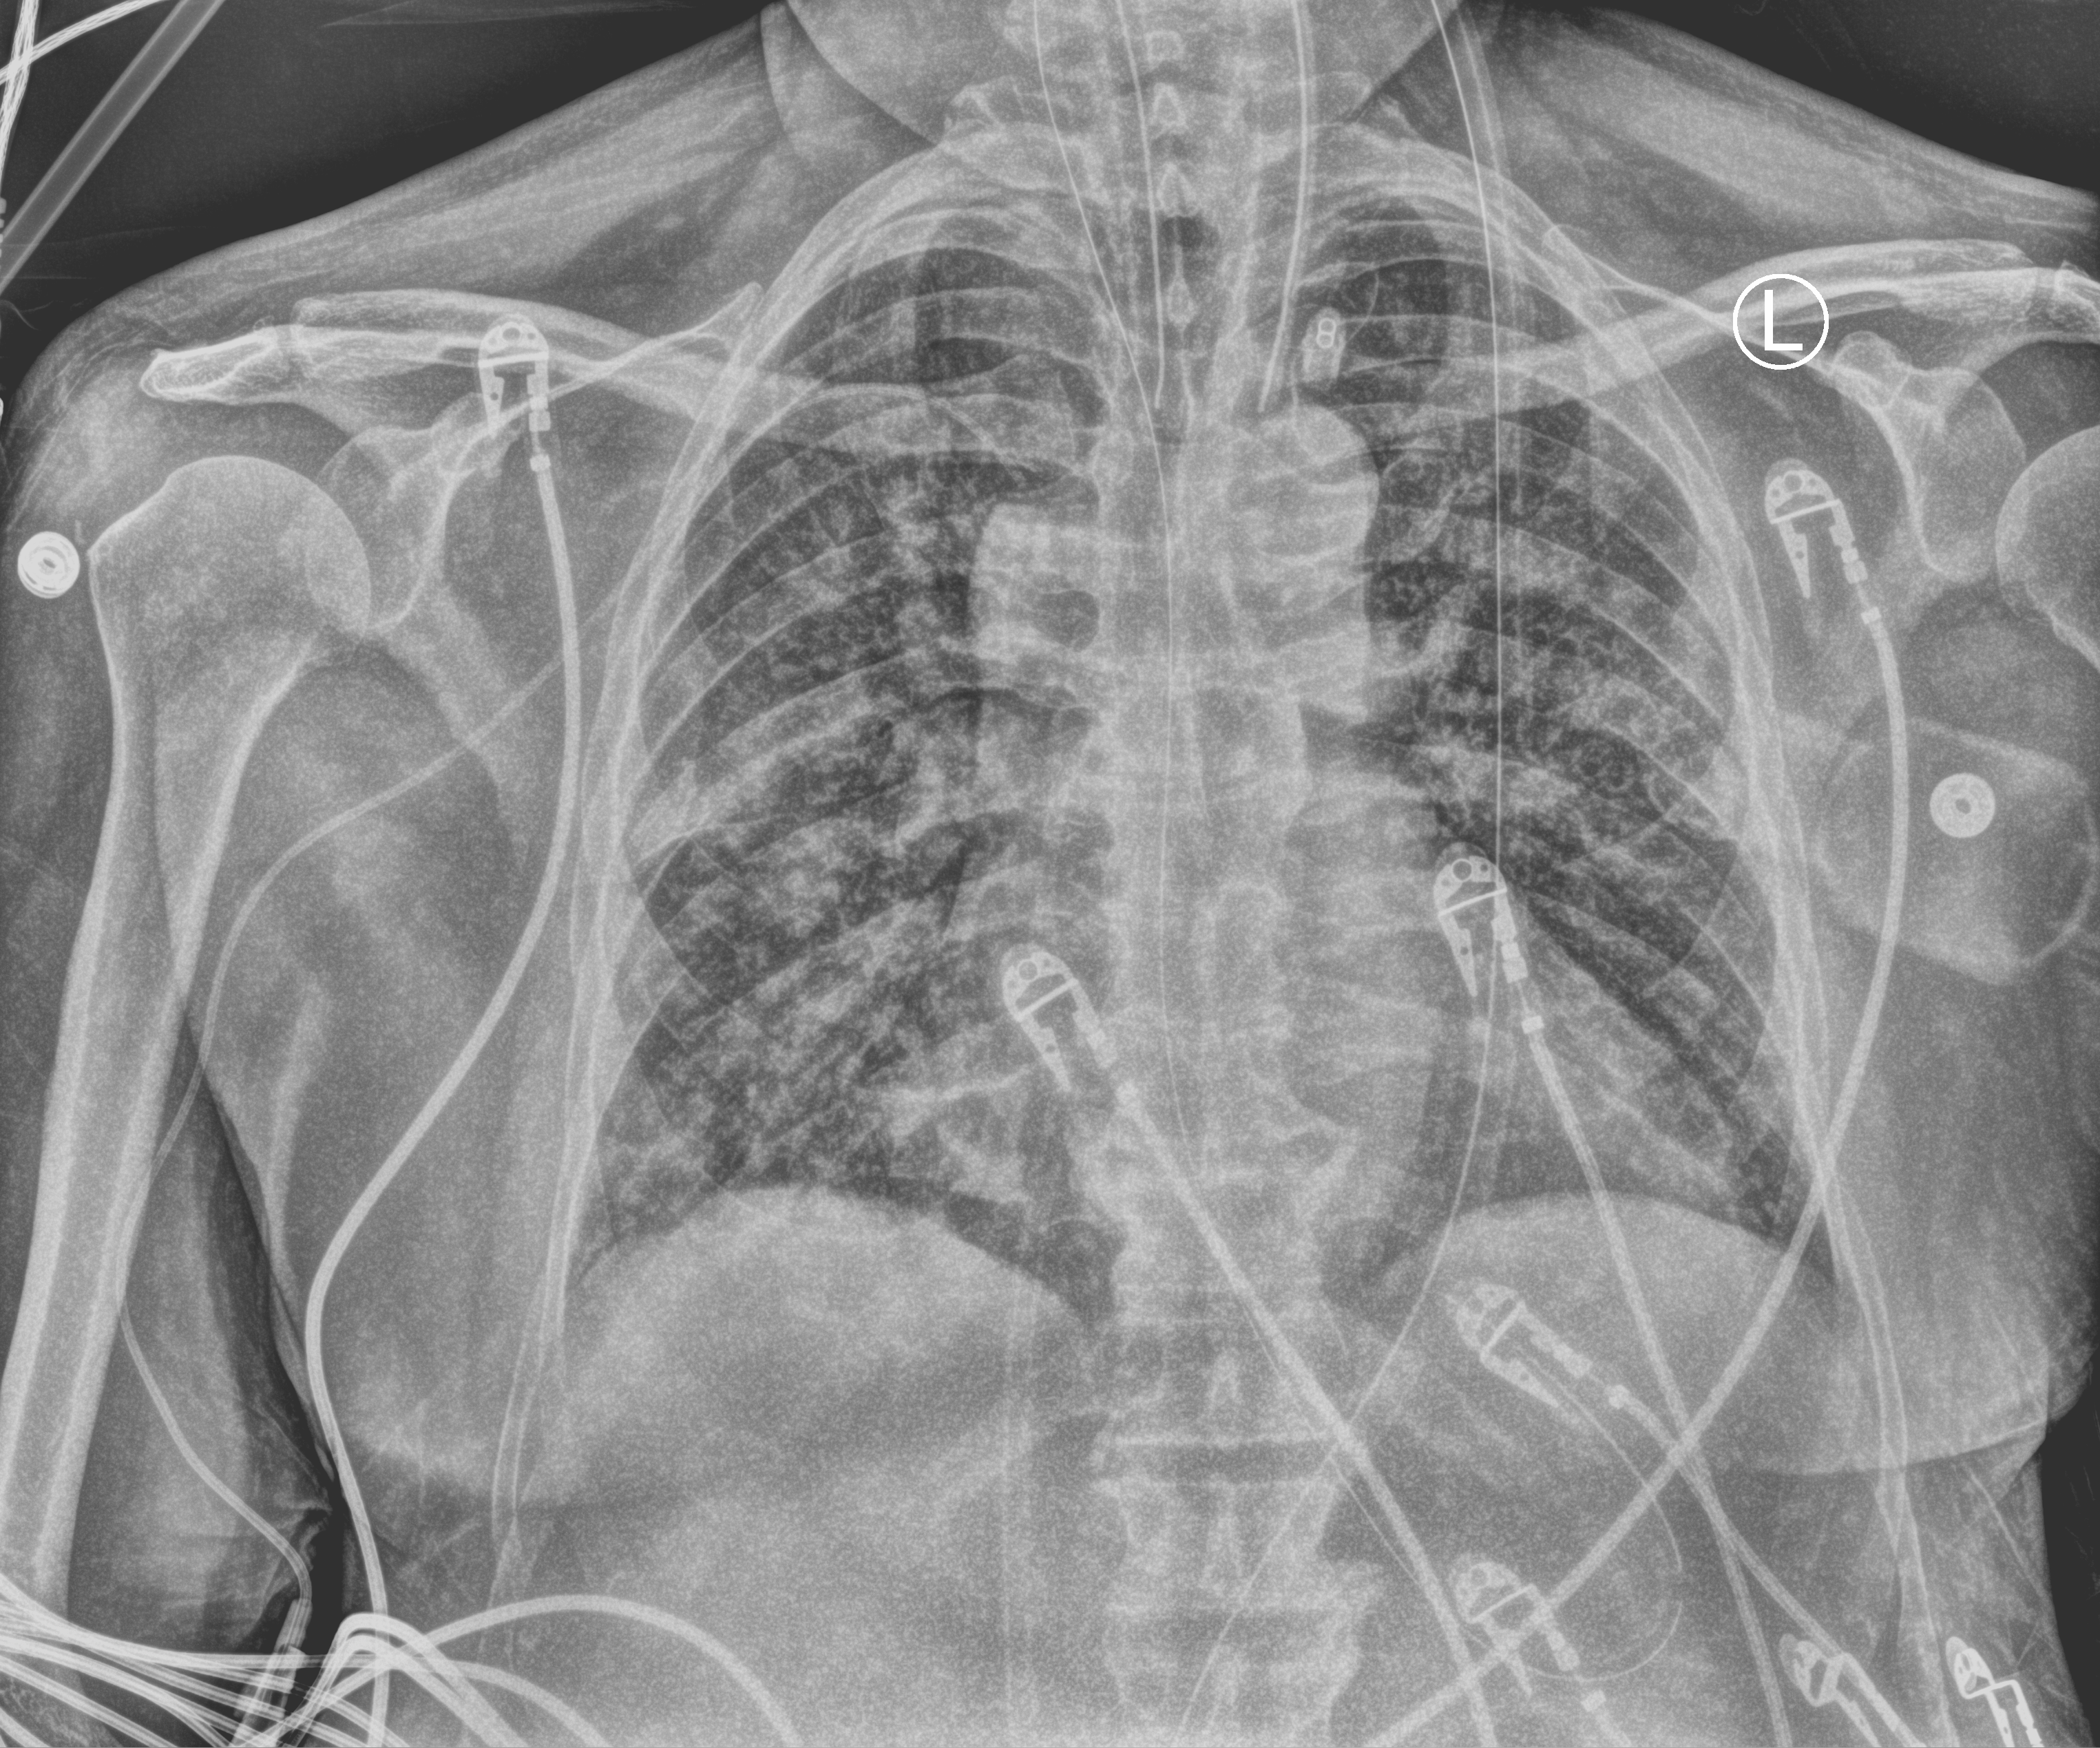
Portable chest radiograph, anteroposterior (AP) projection. Male patient hospitalised with COVID-19, age 60–74 years.
From the hospital-stay record, not from the radiograph (when in the stay this image was taken is not recorded):
- diabetes (admission record): no